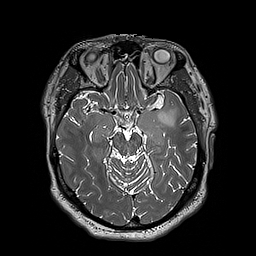
Brain MRI from a brain-tumour surgery series, one axial slice; slice 121 of 192 in the series (ordered by position); 1 mm slice thickness; 256 × 256 image matrix. Case-level facts recorded for this patient, not image findings: histopathology: Astrocytoma; WHO grade: 3; IDH mutation: yes.
Structures marked on this image (outlined manually by an expert reader):
- tumour: box from (x=155, y=107) to (x=174, y=126) px